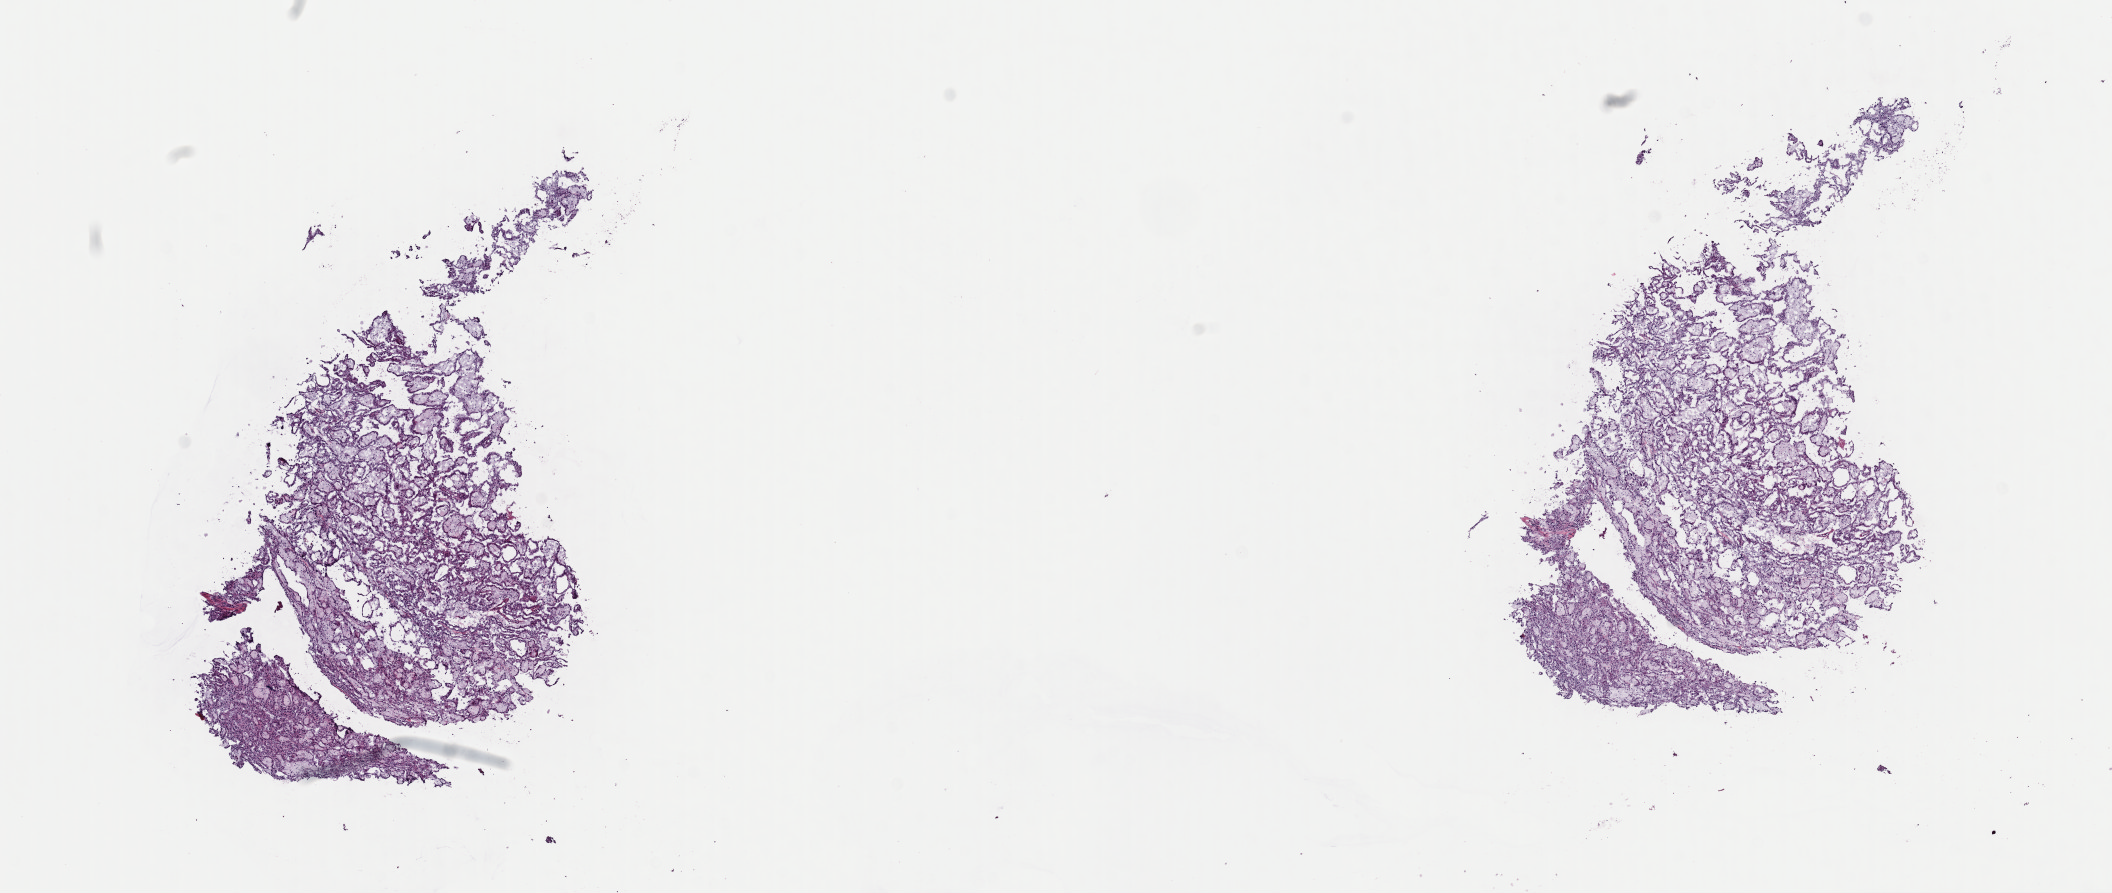
Whole-slide histology image, H&E-stained — a low-resolution overview of the entire scanned area, about 16.7 x 7.1 mm; frozen section from the top of the tissue portion; primary tumour sample from the kidney. Patient: female, age at initial diagnosis 65 years. Composition of this section per pathologist review: tumour cells 100%, tumour nuclei 80%, normal cells 0%, stromal cells 0%, necrosis 0%. Inflammatory infiltration, as recorded: lymphocyte infiltration 1%, monocyte infiltration 3%, neutrophil infiltration 0%.
Laterality: right. Histologic diagnosis: Papillary adenocarcinoma, NOS. AJCC pathologic stage: II (7th edition).